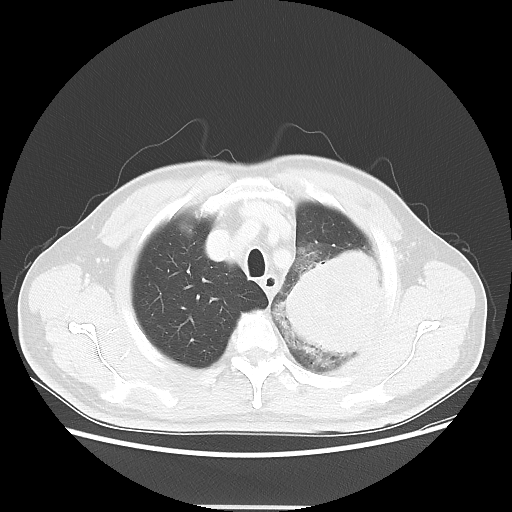
Chest CT, one axial slice; position 46 of 53 along the scan axis; 100 kVp; lung window (W 1500 / L -600 HU); 5 mm slice thickness; 512 × 512 image matrix, field of view 391 × 391 mm. Patient: male, 60 years. Case-level facts recorded for this patient, not image findings: clinical TNM (as recorded): T4 N1 M1a.
Outlined on this slice (rectangle marked by the reading radiologist):
- lung tumour (recorded histology: large cell carcinoma): bounding box <284,248,383,368> (left, top, right, bottom; pixels)